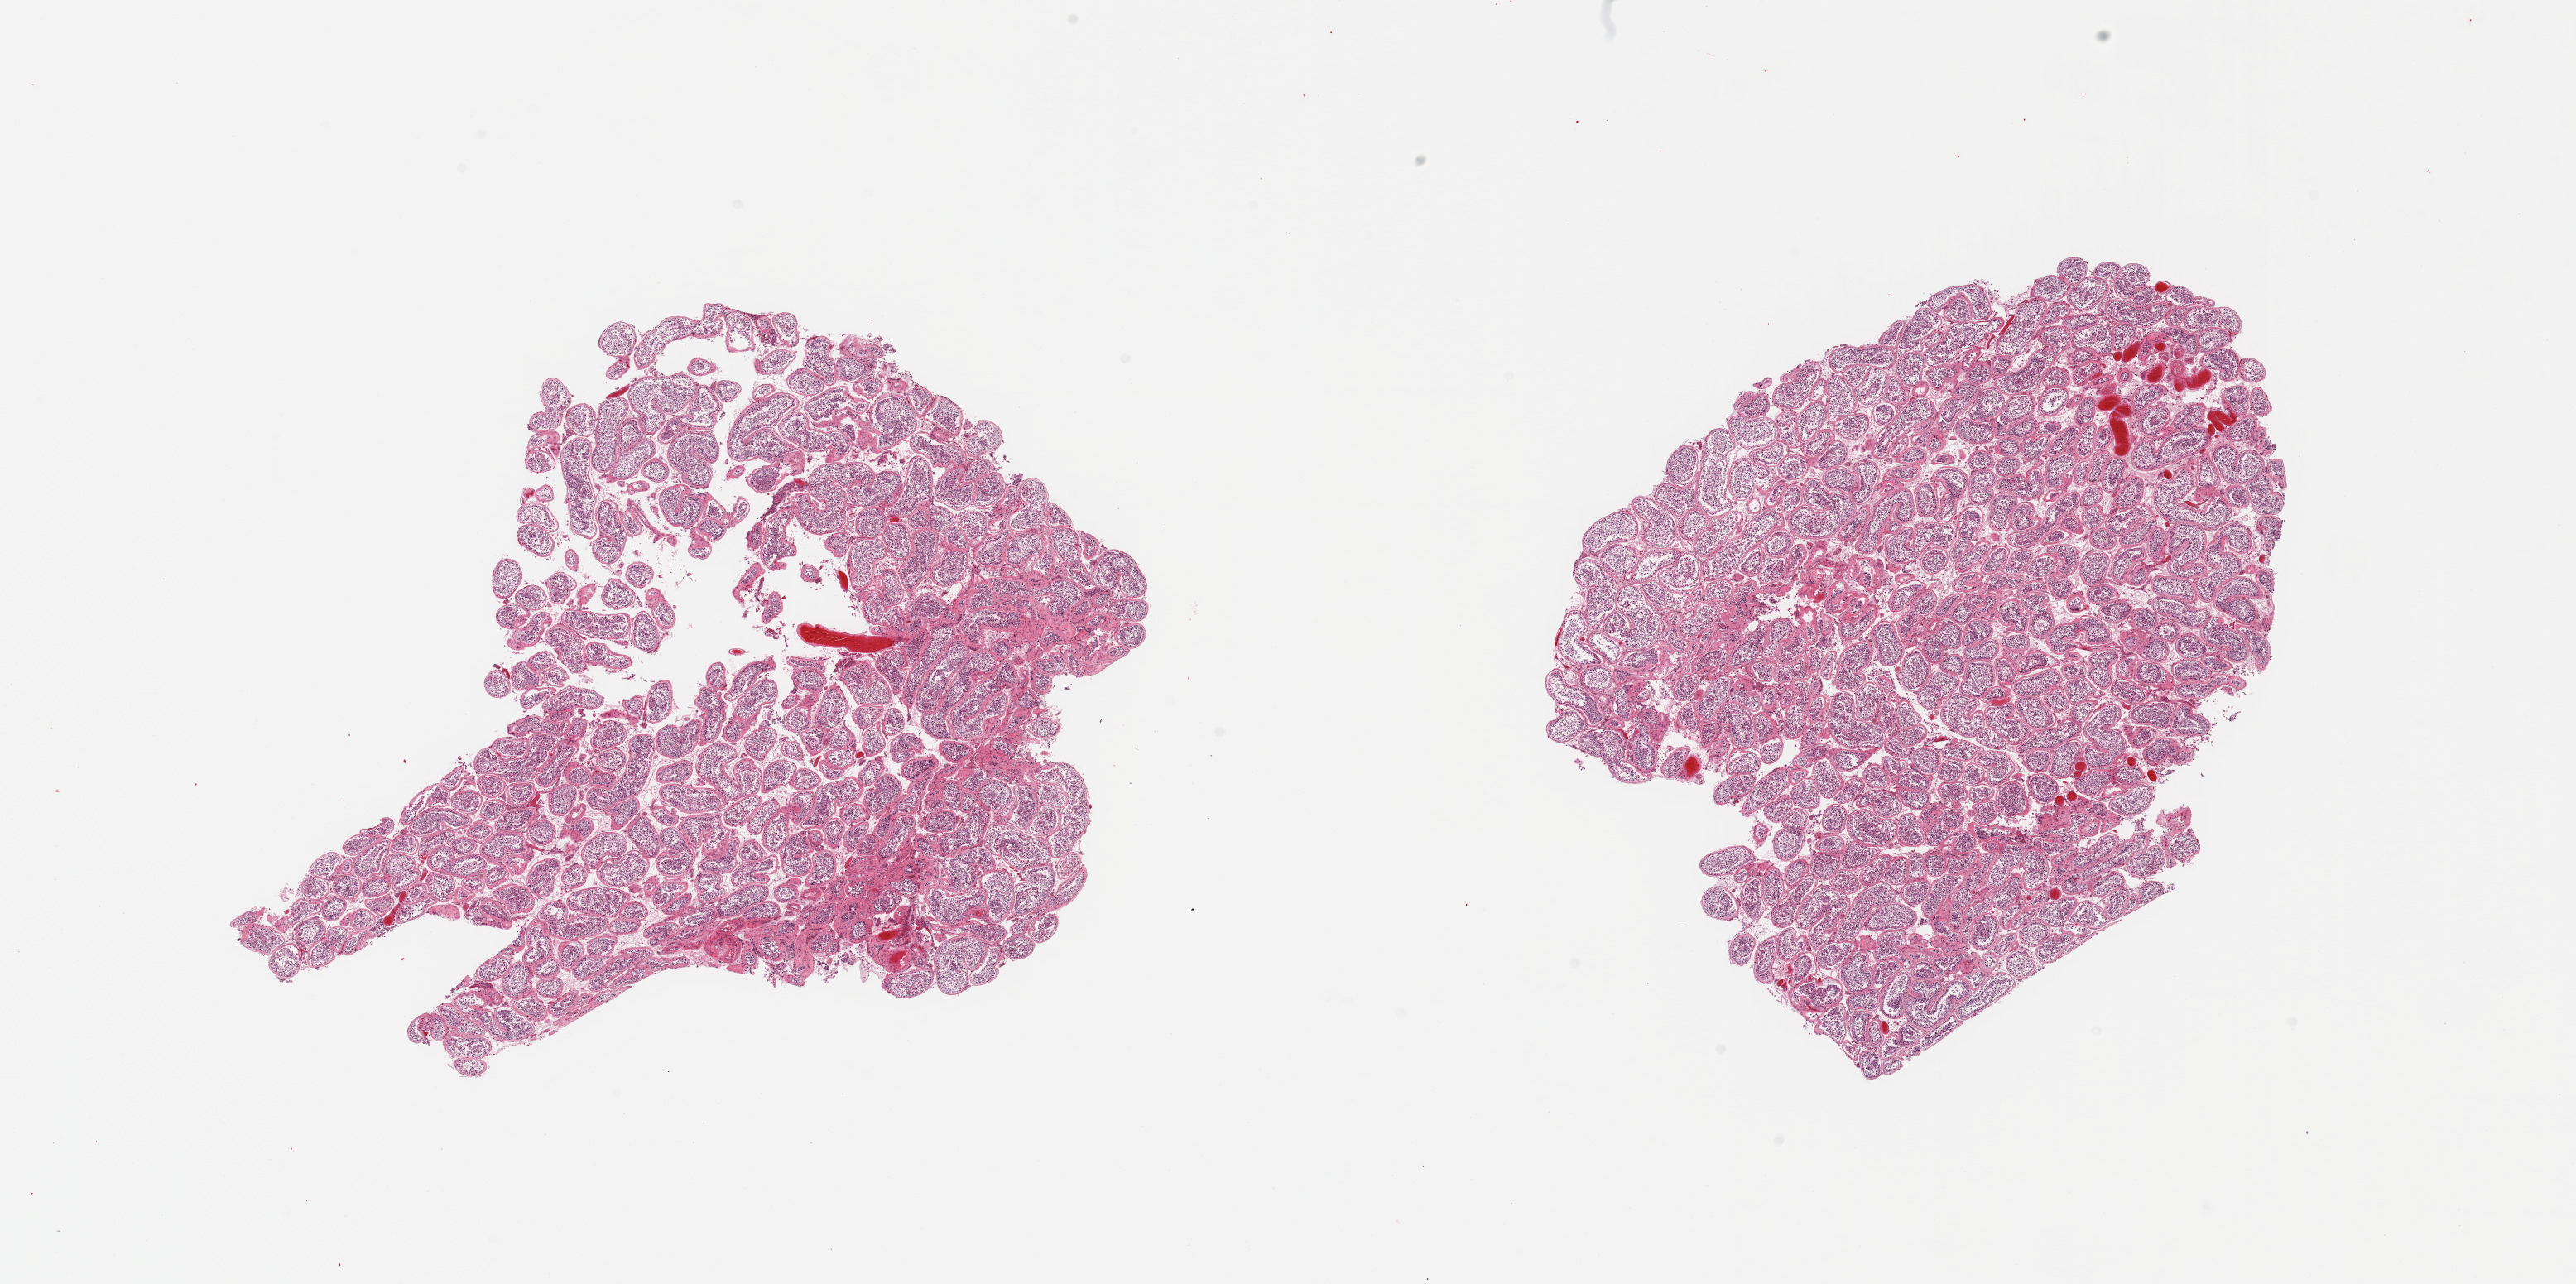
Haematoxylin and eosin whole-slide image, shown as a low-resolution overview of the whole scanned area (about 24.6 x 12.3 mm, slide scanned at 20x). PAXgene-fixed paraffin-embedded (PFPE) section. Section of testis (target tissue). Donor tissue sample. Donor sex: male.
• reviewer comment on this tissue sample: 2 pieces, spermatogenesis present but appears reduced